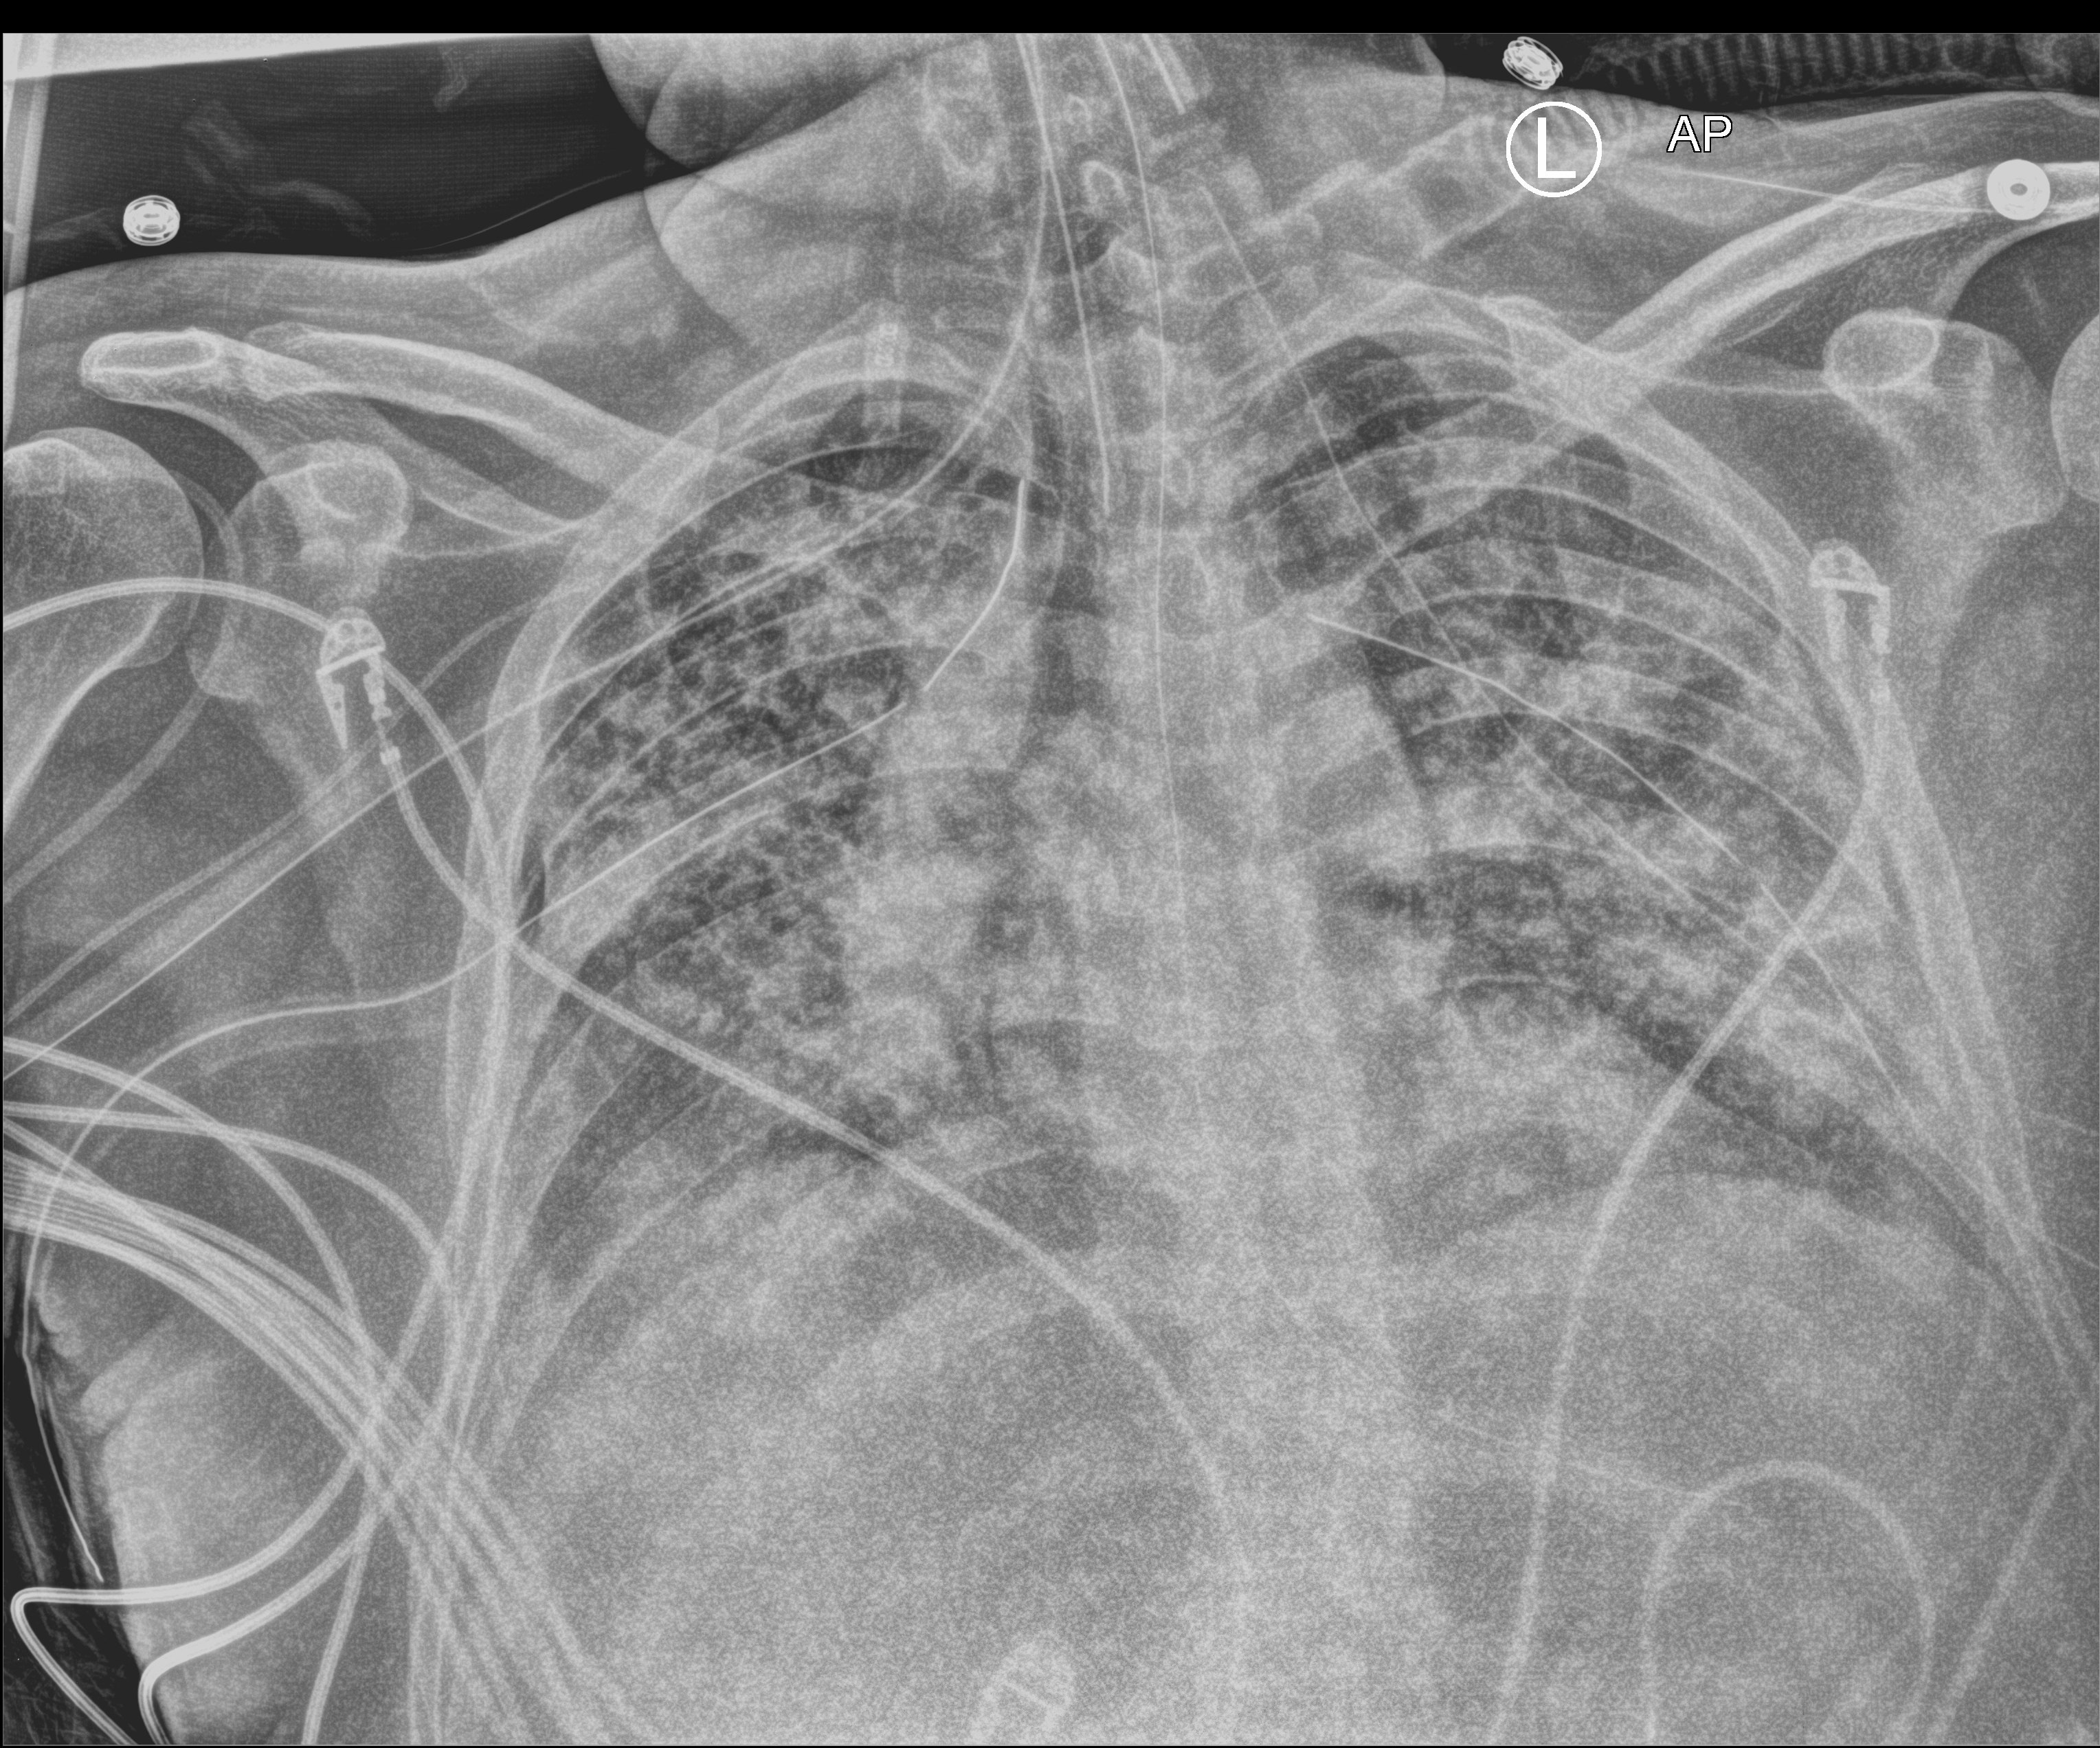
Portable chest radiograph; anteroposterior (AP) projection. Patient hospitalised with COVID-19; male, aged 18–59 years.
Hospital-stay facts (about this admission, not read from this image; timing relative to this image not recorded):
- smoking status (admission record): never
- admitted to intensive care during this hospital stay: yes
- length of hospital stay: 63 days